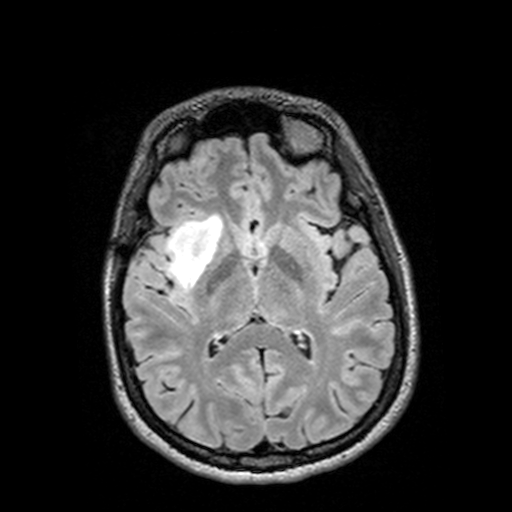
Brain MRI from a brain-tumour surgery series, one axial slice. Slice 69 of 144 in the series (ordered by position). T2 FLAIR. 1 mm slice thickness. 512 × 512 image matrix. Case-level facts recorded for this patient, not image findings: histopathology: Astrocytoma; WHO grade: 3; IDH mutation: yes; tumour location: Right Insular Temporal.
Annotated regions visible in this slice (expert manual segmentation):
- tumour: bounding box [x1, y1, x2, y2] px = [126, 213, 232, 292]